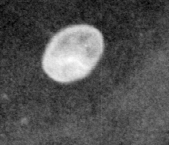
Crop from a digitized film mammogram around one marked abnormality, right breast, MLO view.
- Finding: calcifications, morphology round and regular / lucent center / punctate, distribution diffusely scattered; BI-RADS assessment category 2; benign without callback (not worked up further).